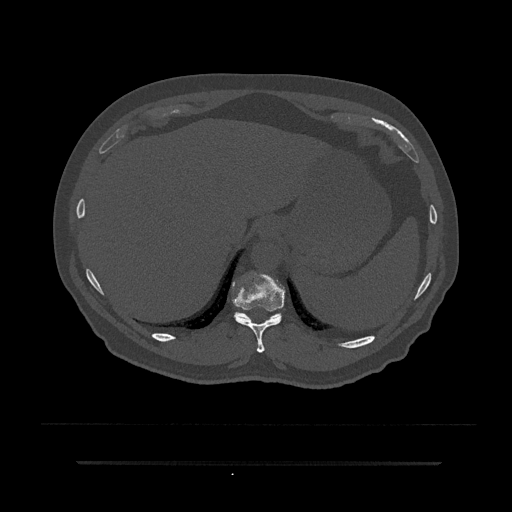
CT including the spine, one axial slice; slice 309 of 797 in the series (ordered by position); 120 kVp; bone window (W 1800 / L 400 HU); 0.5 mm slice thickness; 512 × 512 image matrix, field of view 464 × 464 mm. Male patient, age 59 years. Case-level facts recorded for this patient, not image findings: primary cancer: bile ducts; vertebrae with lytic lesions (as recorded): T10.
Structures marked on this image (semi-automatically segmented with operator editing):
- T10 vertebra: bounding box [x1, y1, x2, y2] px = [232, 273, 285, 353]
- T11 vertebra: [234, 312, 282, 321]